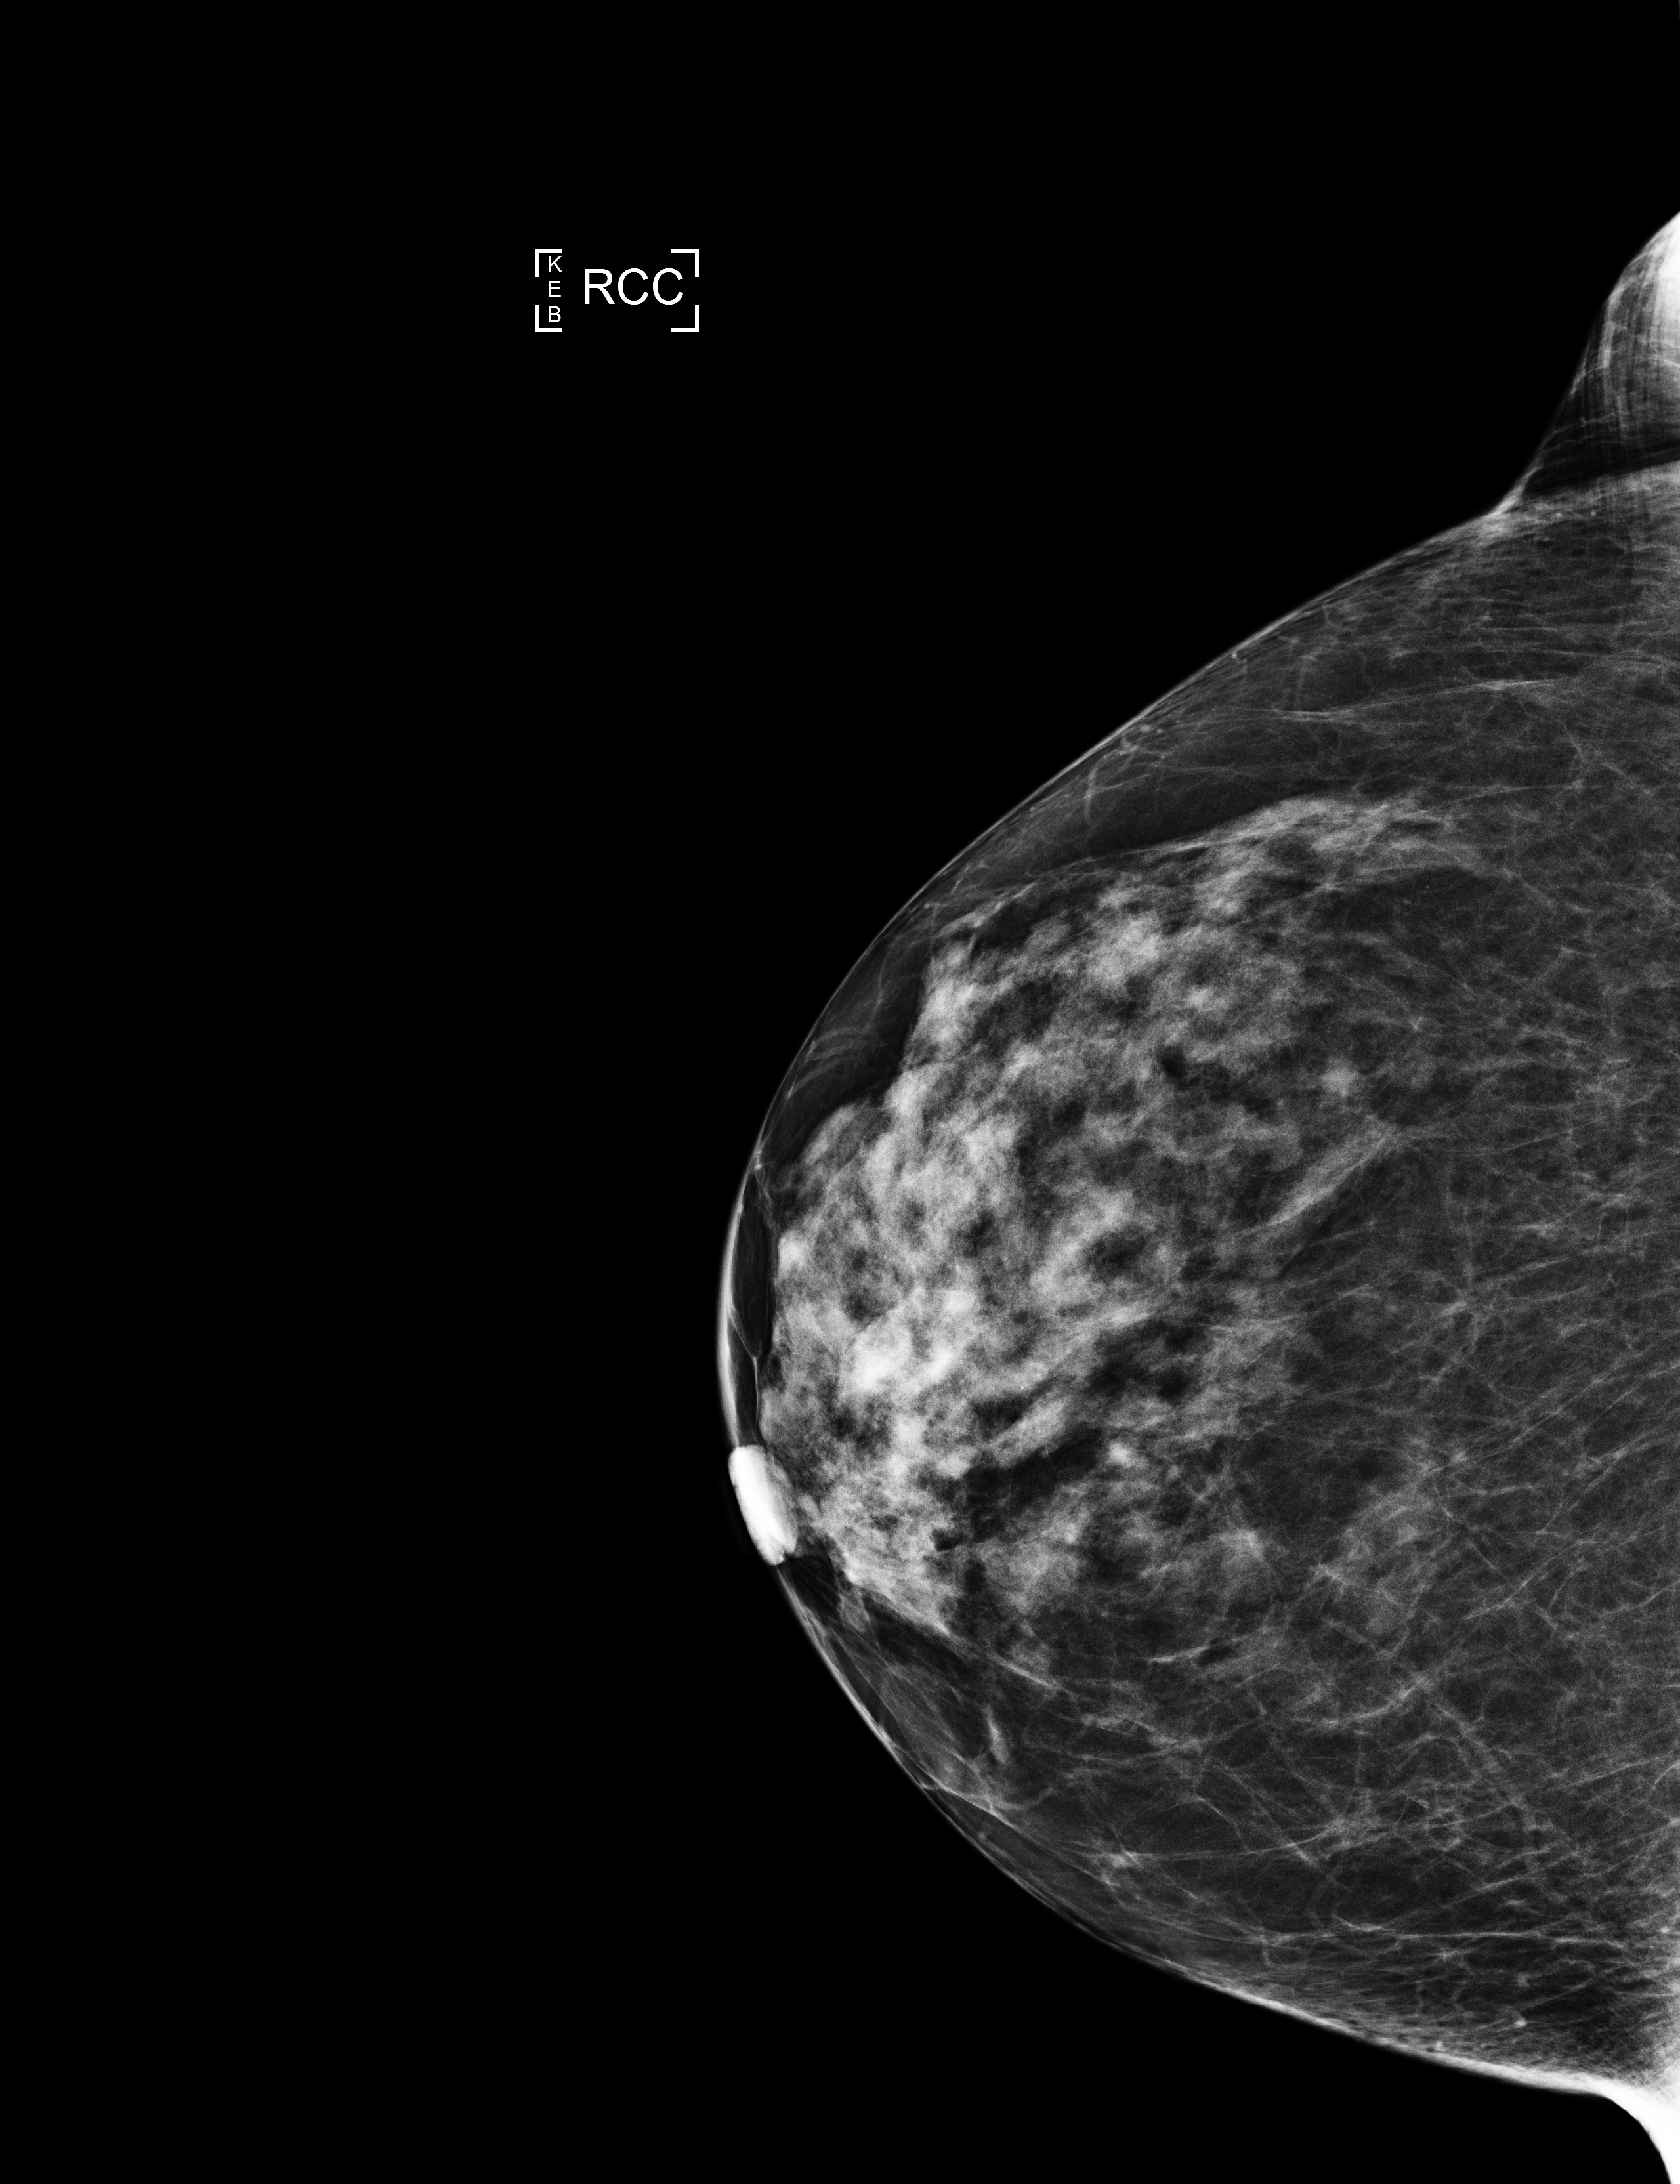
Annual screening mammography examination. Female patient, age 73 years.
Image type: full-field digital mammogram. Breast: right. Projection: CC view.